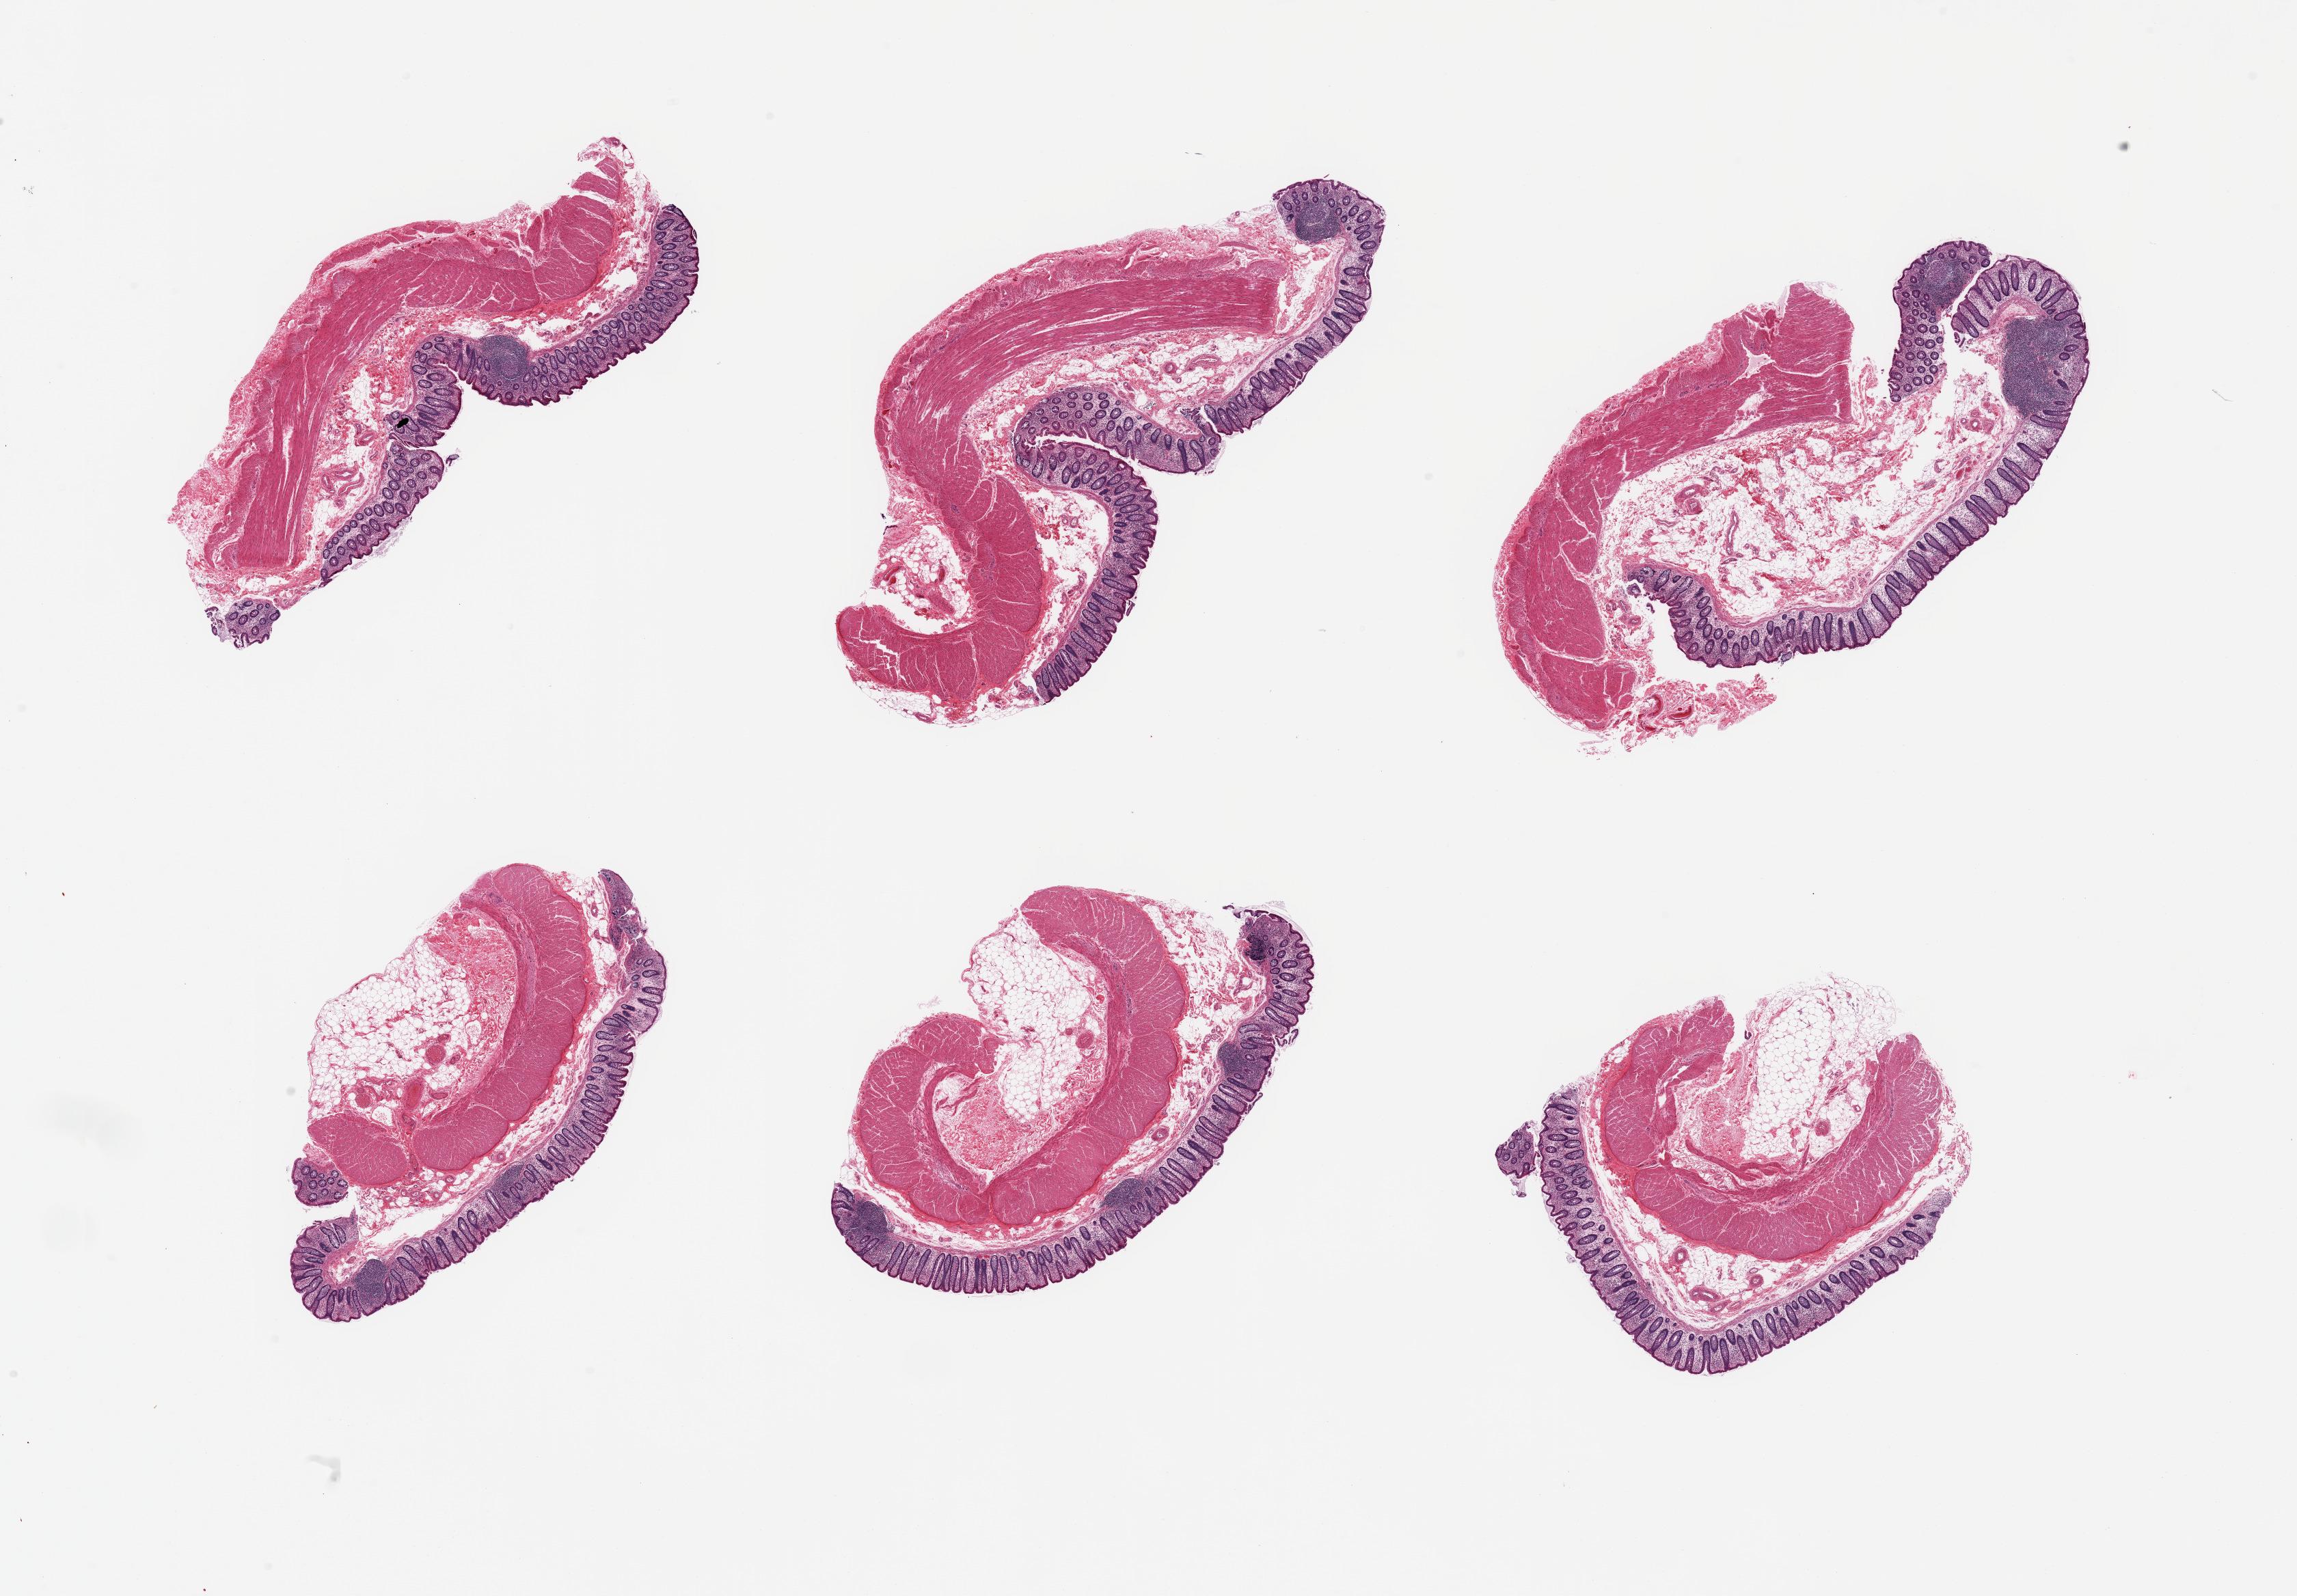
Whole-slide image, H&E stain, whole scanned area (about 26.6 x 18.5 mm) shown as a low-resolution overview, PAXgene-fixed paraffin-embedded (PFPE) section, target tissue: transverse colon, donor tissue sample. Donor: male.
Pathologist's review note for this sample: 6 pieces; mucosa well preserved; 3 pieces have abundant perimuscular fat.